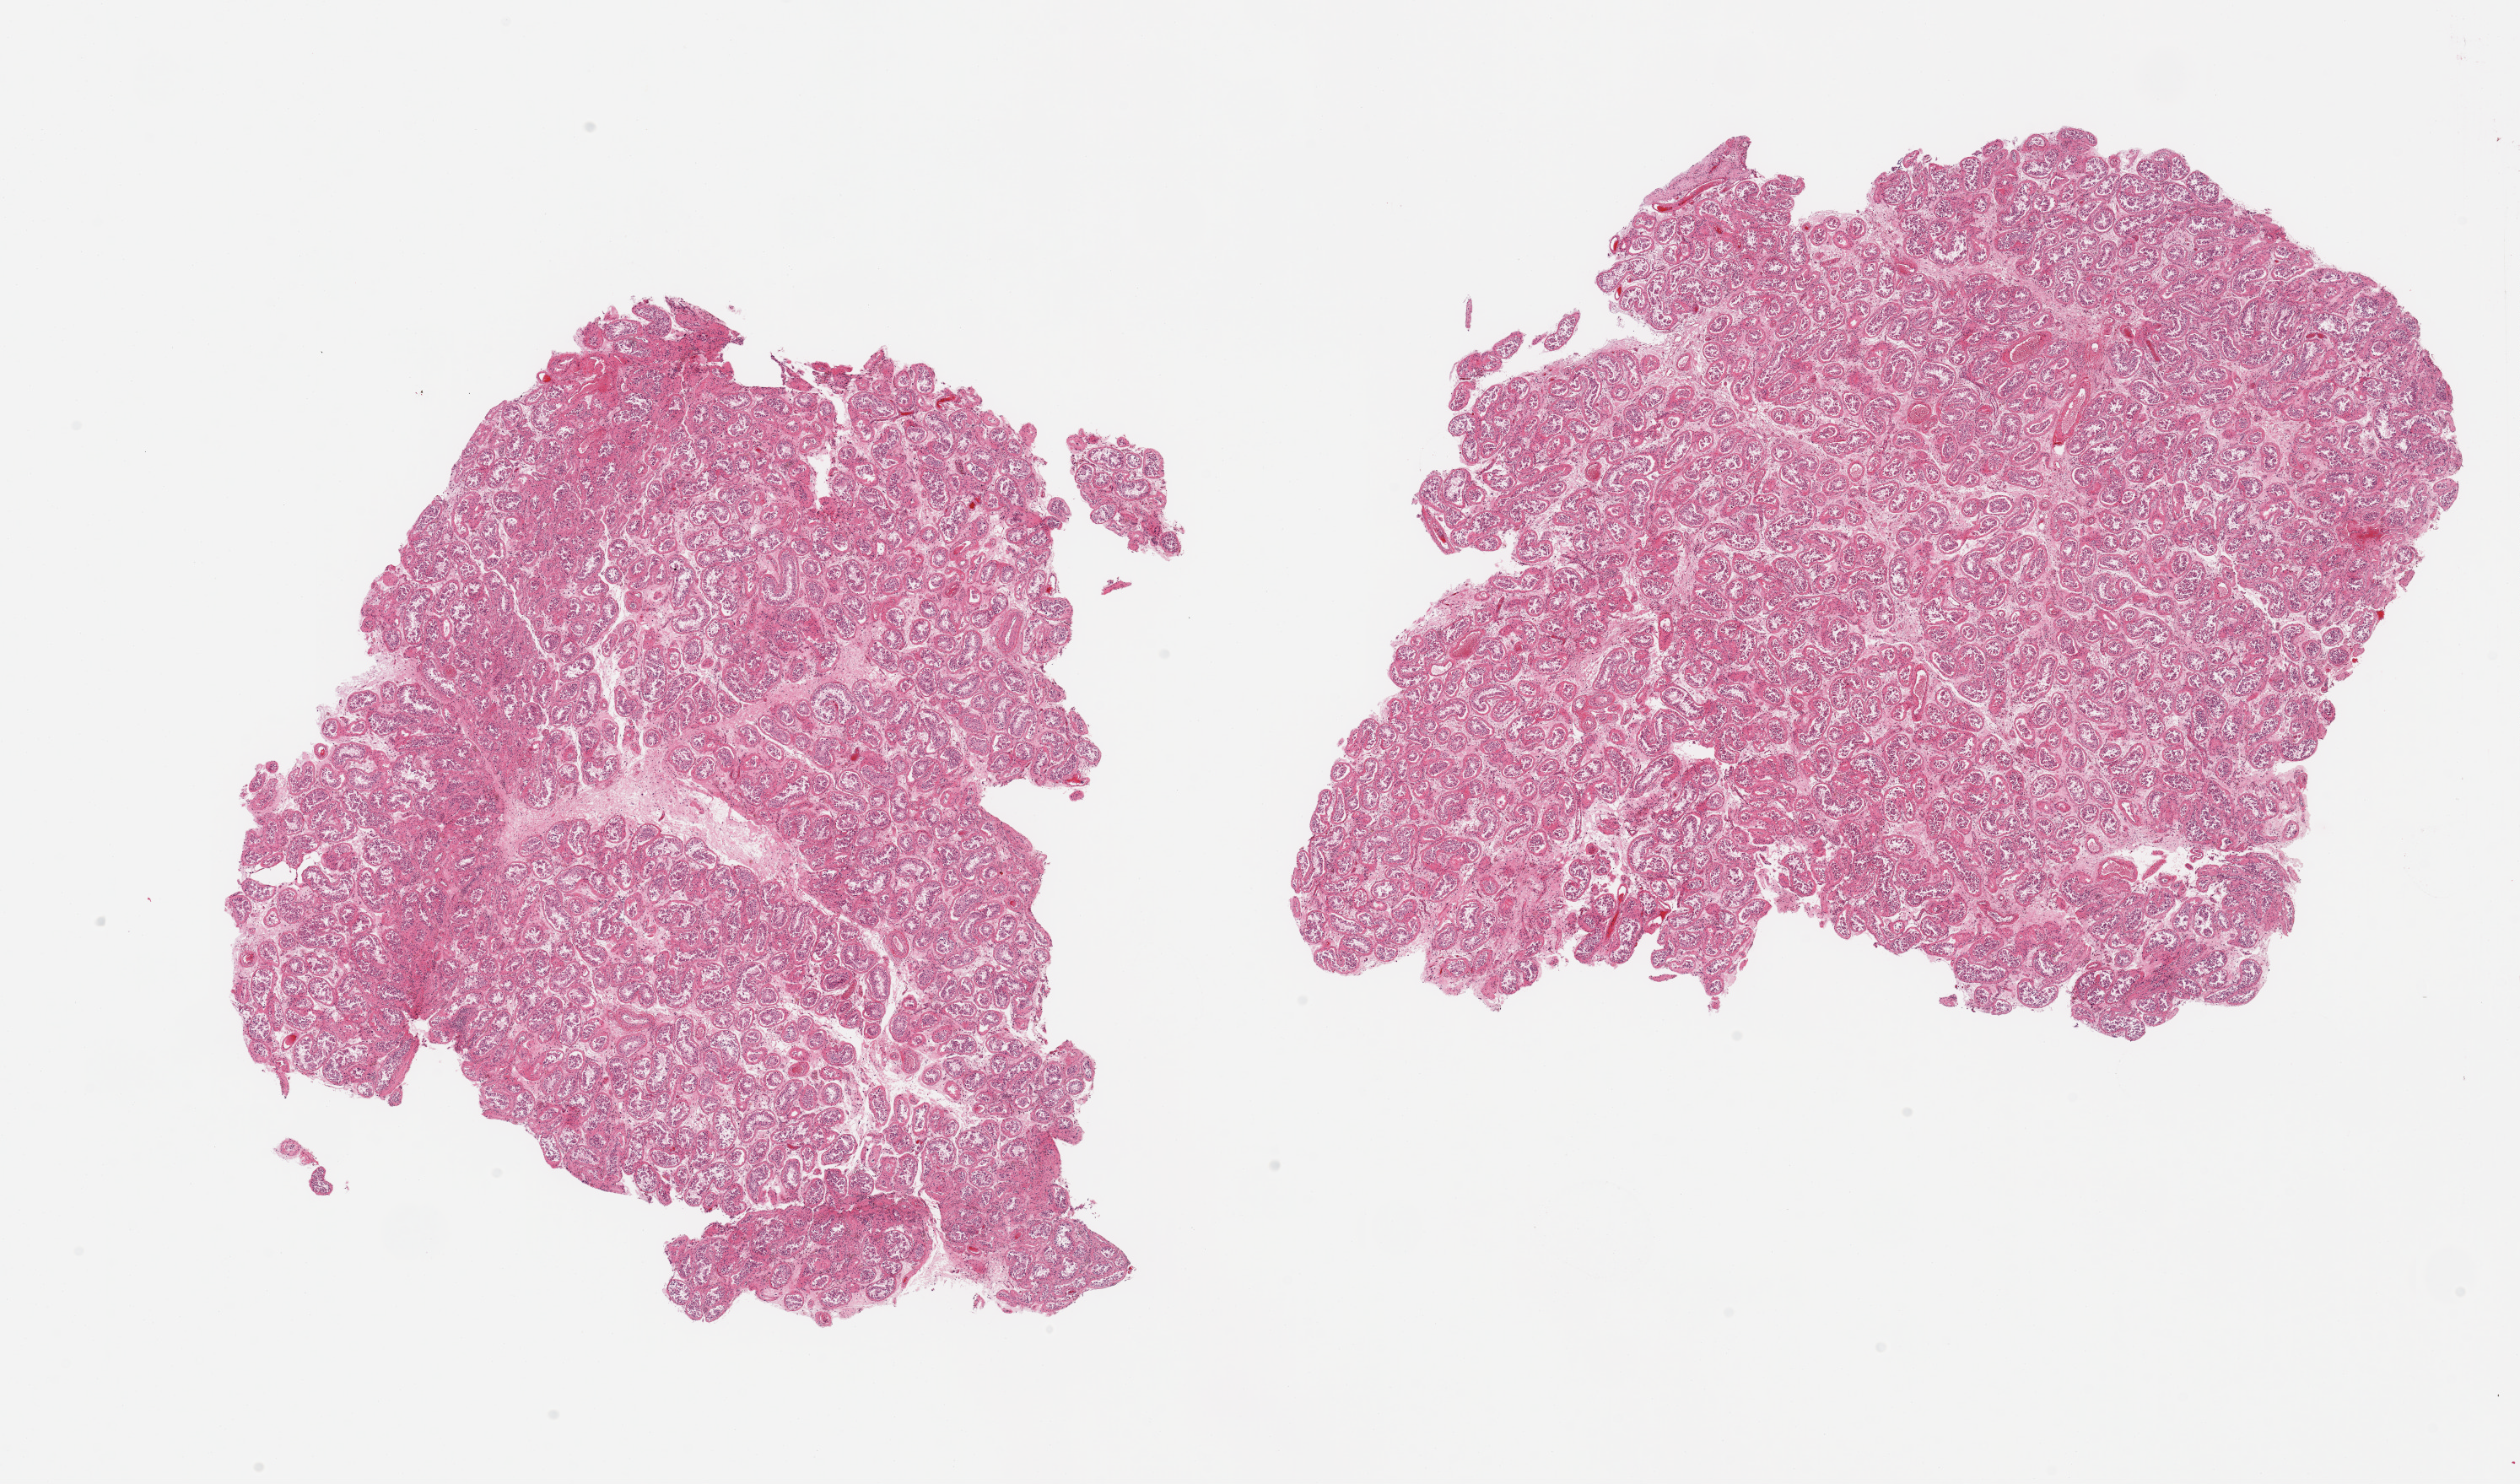
Whole-slide image, haematoxylin and eosin stain, a low-resolution overview of the entire scanned area, about 23.6 x 13.9 mm (slide scanned at 20x). PAXgene-fixed paraffin-embedded (PFPE) section. Sampled site (target tissue): testis. Donor tissue sample.
• reviewer comment on this tissue sample: 2 pieces; arrested spermatogenesis with spared Sertoli cells; peritubular fibrosis